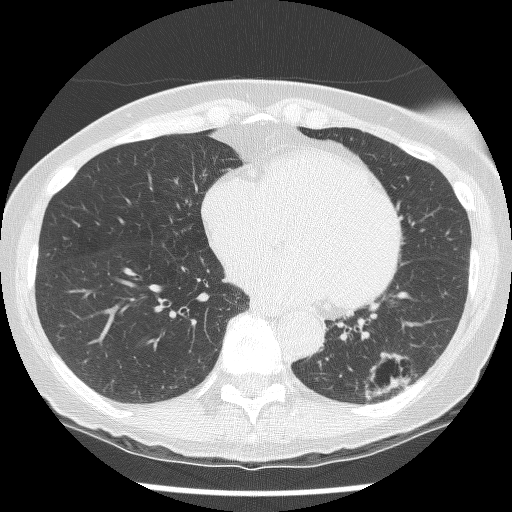
Chest CT (low-dose screening protocol), one axial image, second annual screen, lung window (W 1500 / L -600 HU), 2.5 mm slice thickness, lung (sharp) reconstruction kernel (BONE), slice 84 of 136 in the series. Female participant, aged 61 years at enrolment.
Expert reader's lesion annotation, box from (x=334, y=334) to (x=434, y=418) px. The screening reader recorded 2 non-calcified nodules or masses ≥4 mm on this exam (left lower lobe, left lower lobe); which of them this box marks is not recorded. Official screen result: positive, no significant change: stable abnormalities potentially related to lung cancer, unchanged since the prior screening exam.